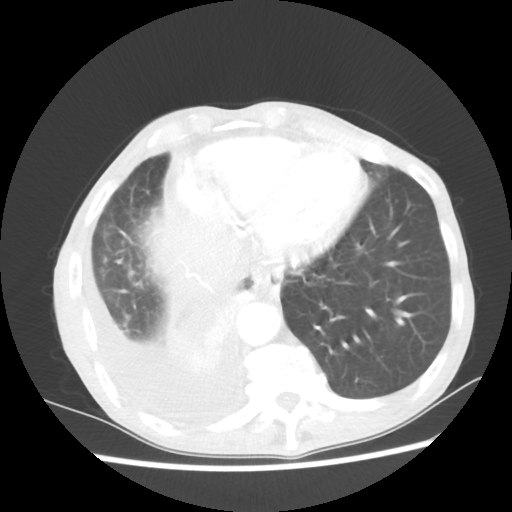
Chest CT, one axial slice; position 16 of 60 along the scan axis; 80 kVp; lung window (W 1500 / L -600 HU); 5 mm slice thickness; 512 × 512 image matrix, field of view 335 × 335 mm. Male patient, age 76 years. Case-level facts recorded for this patient, not image findings: clinical TNM (as recorded): T3 N3 M1a; histopathological grade: G3.
Outlined on this slice (bounding box drawn by a radiologist):
- lung tumour (recorded histology: squamous cell carcinoma): bounding box <162,293,259,375> (left, top, right, bottom; pixels)